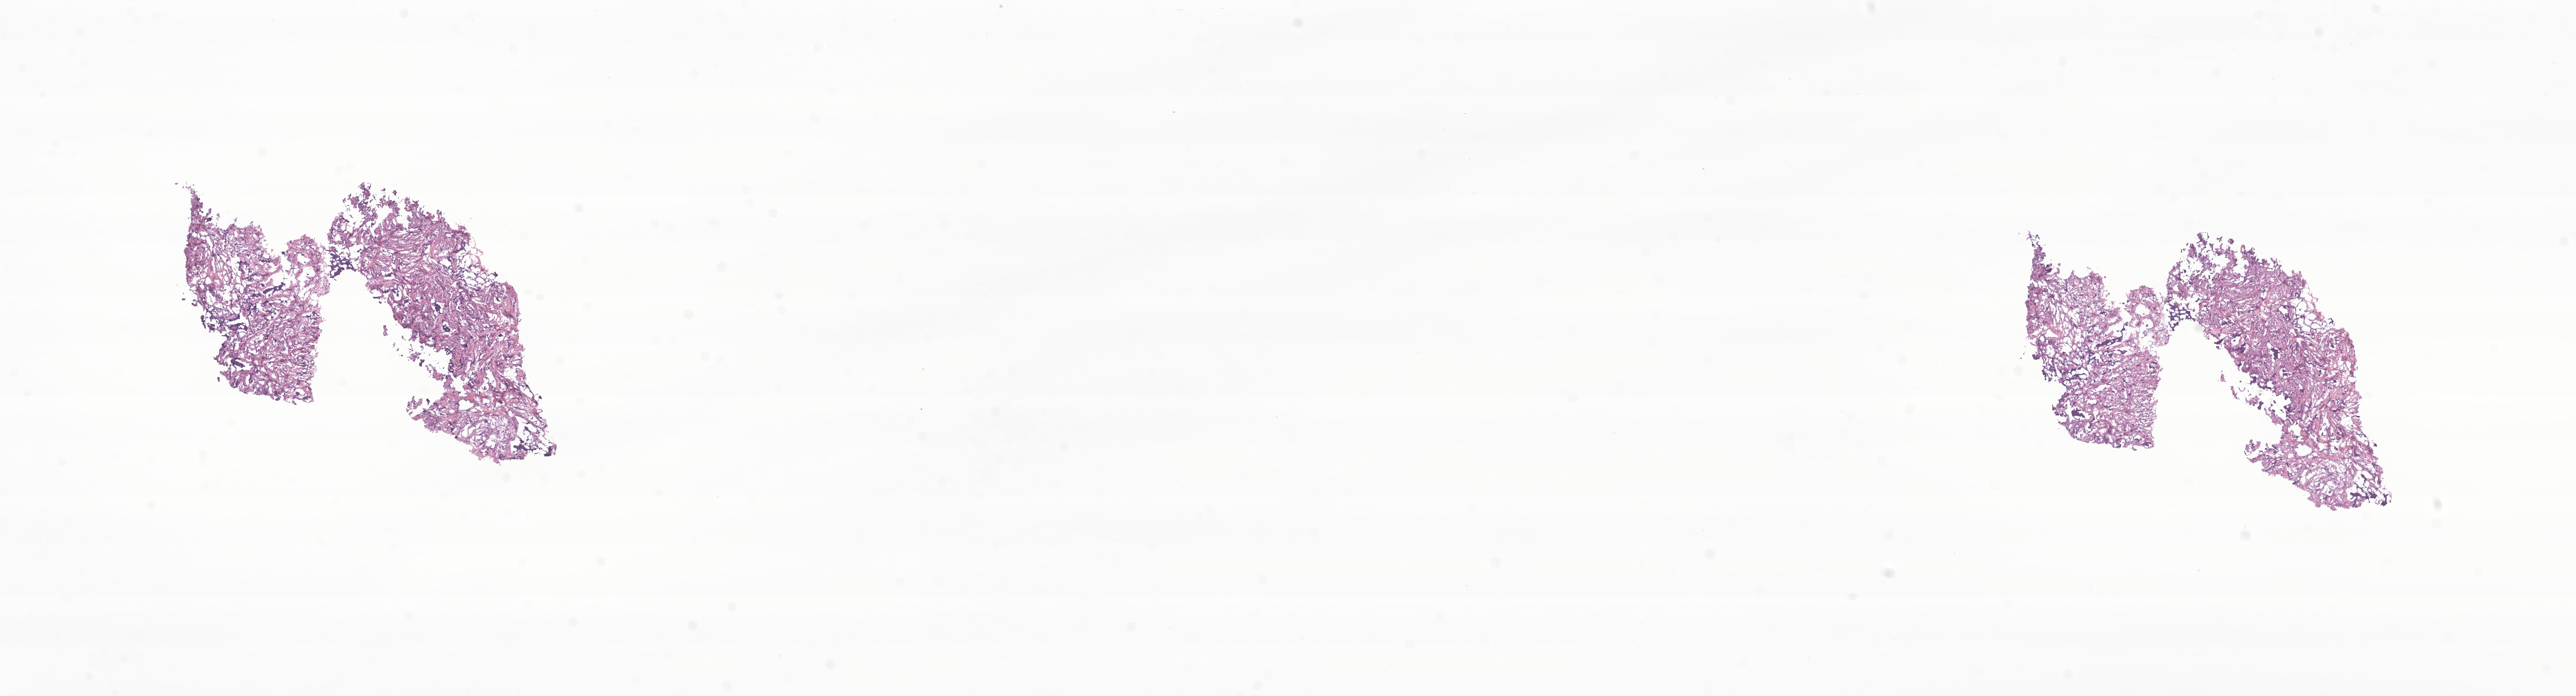
Digitized haematoxylin and eosin-stained section of tumor tissue from the brain — whole scanned area (about 27.4 x 7.4 mm) shown as a low-resolution overview, frozen section. Patient: male, age 60 months (5 years).
* recorded diagnosis: Medulloblastoma, NOS